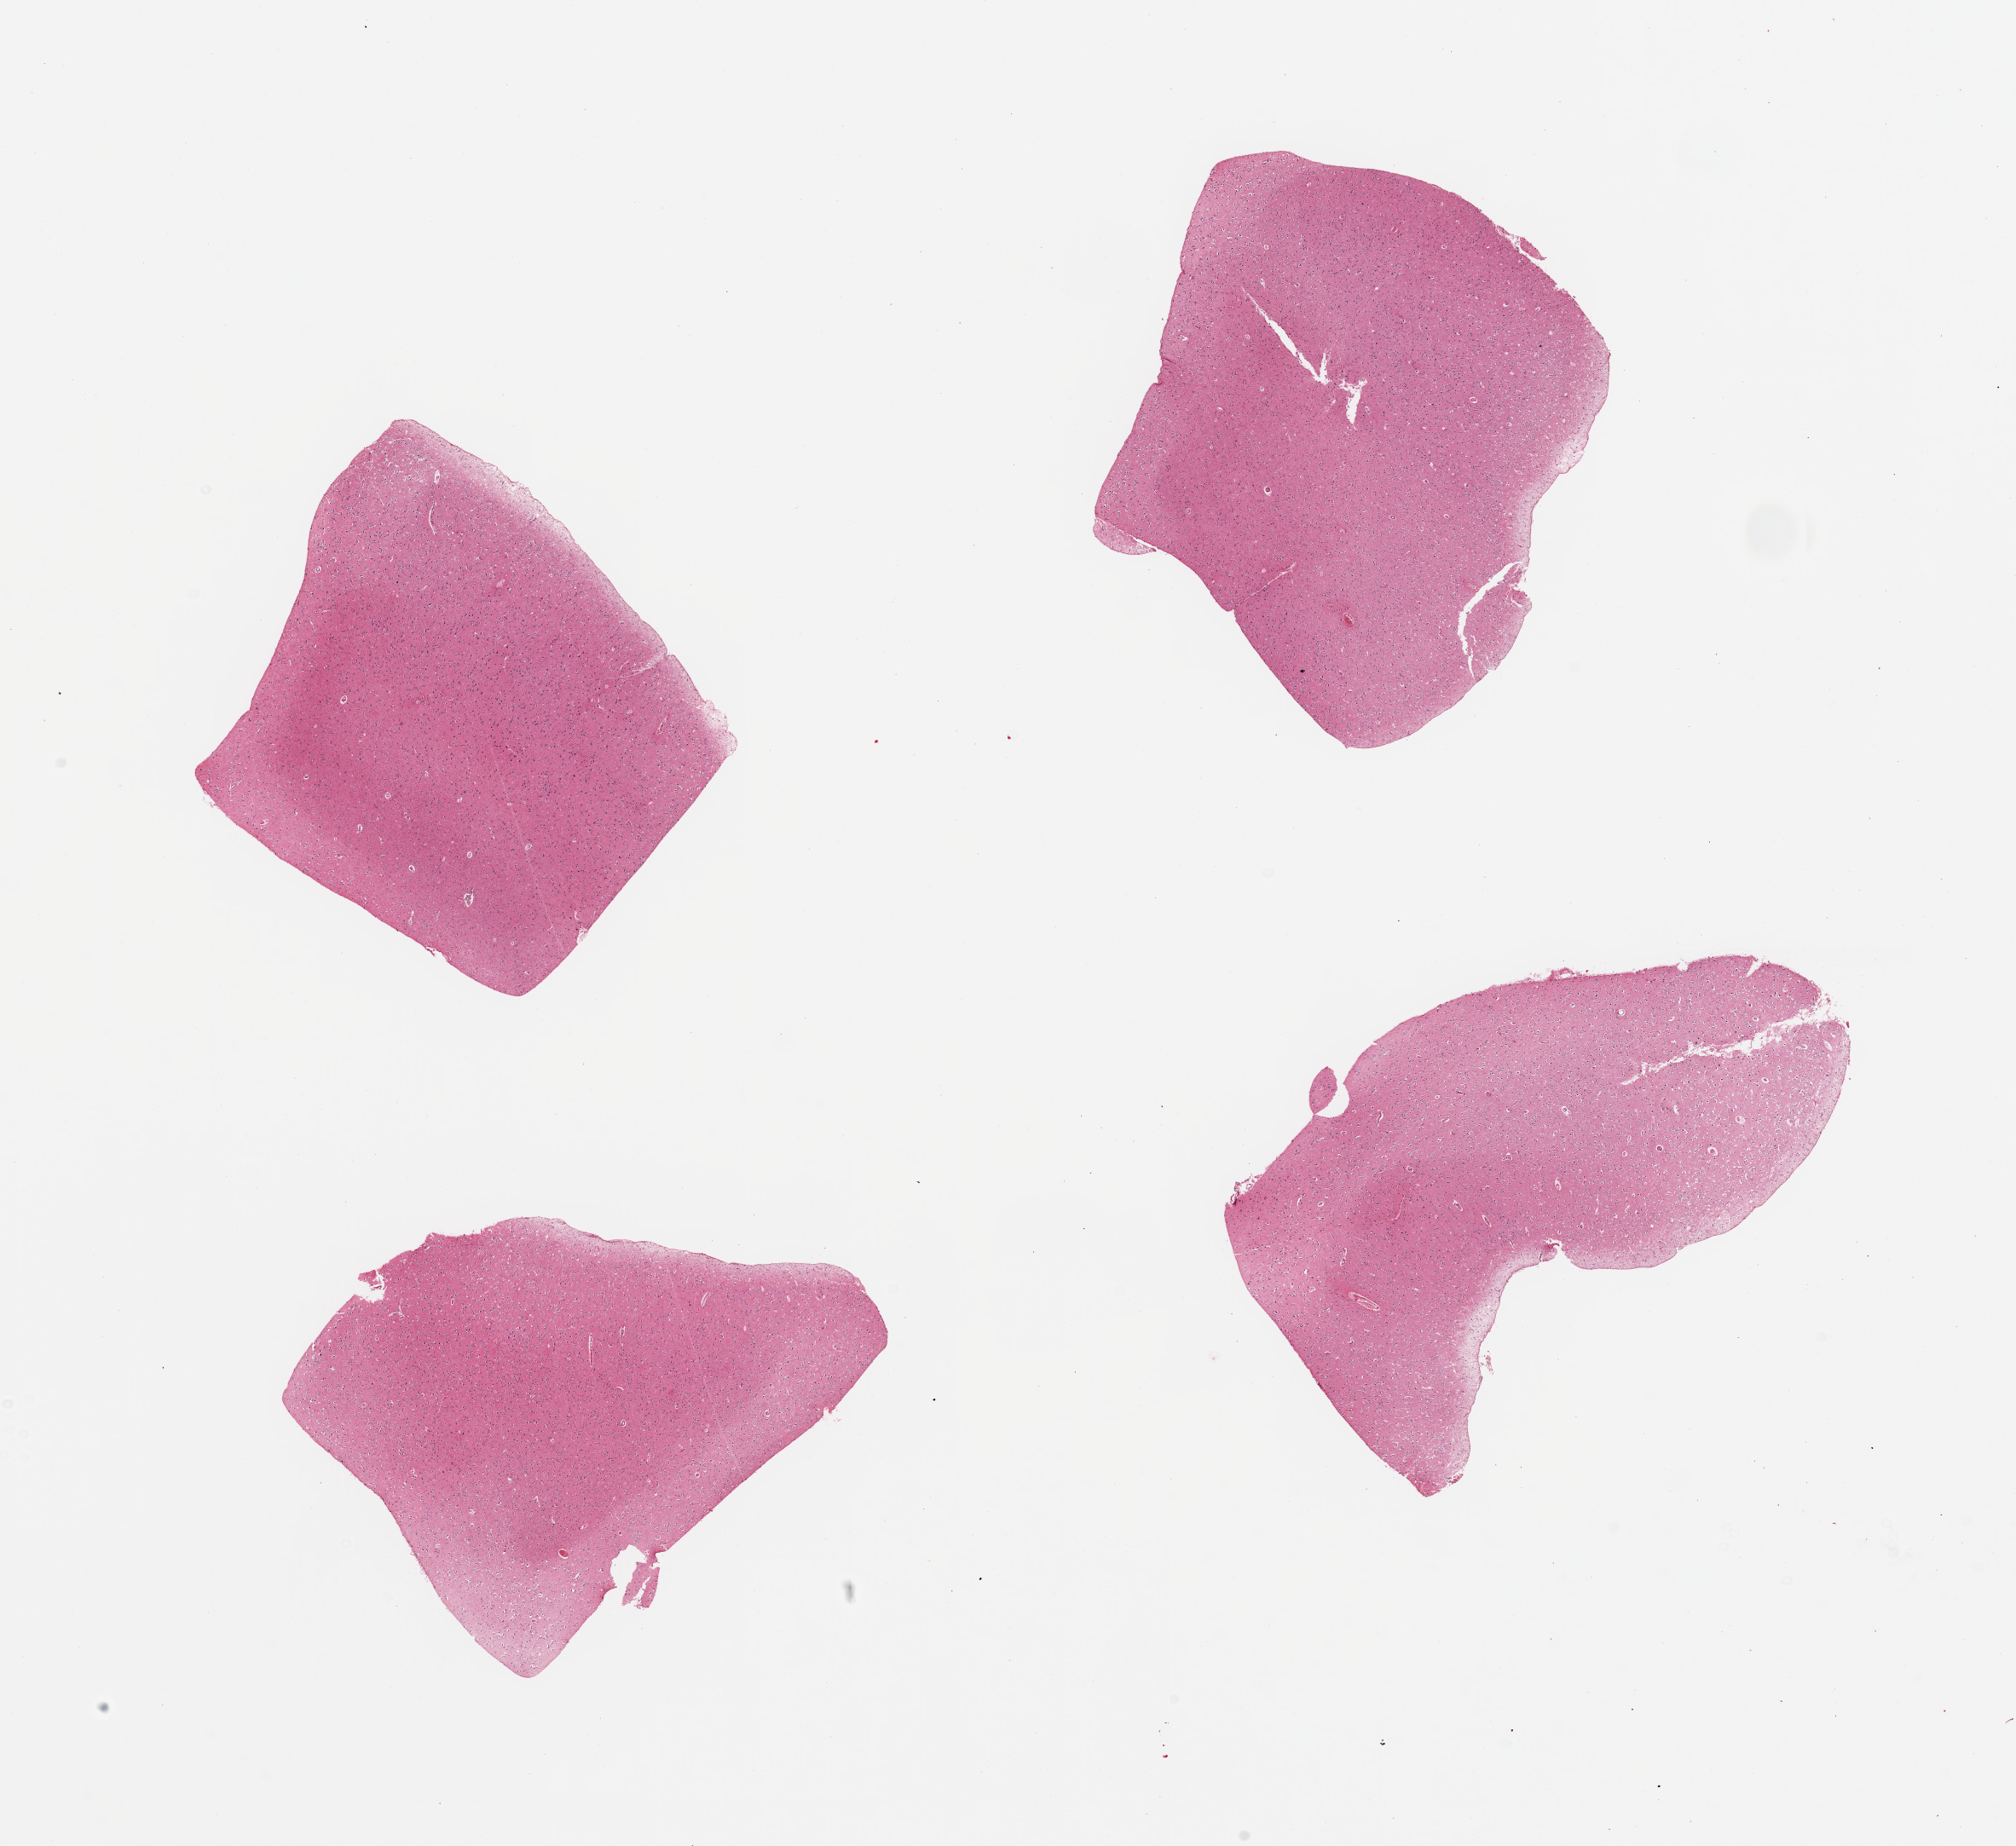
H&E whole-slide image, brightfield — shown as a low-resolution overview of the whole scanned area (about 18.7 x 17.1 mm); PAXgene-fixed, paraffin-embedded tissue; section of cerebral cortex (target tissue); donor tissue sample. Donor sex: male.
Review note (as recorded): 4 pieces.